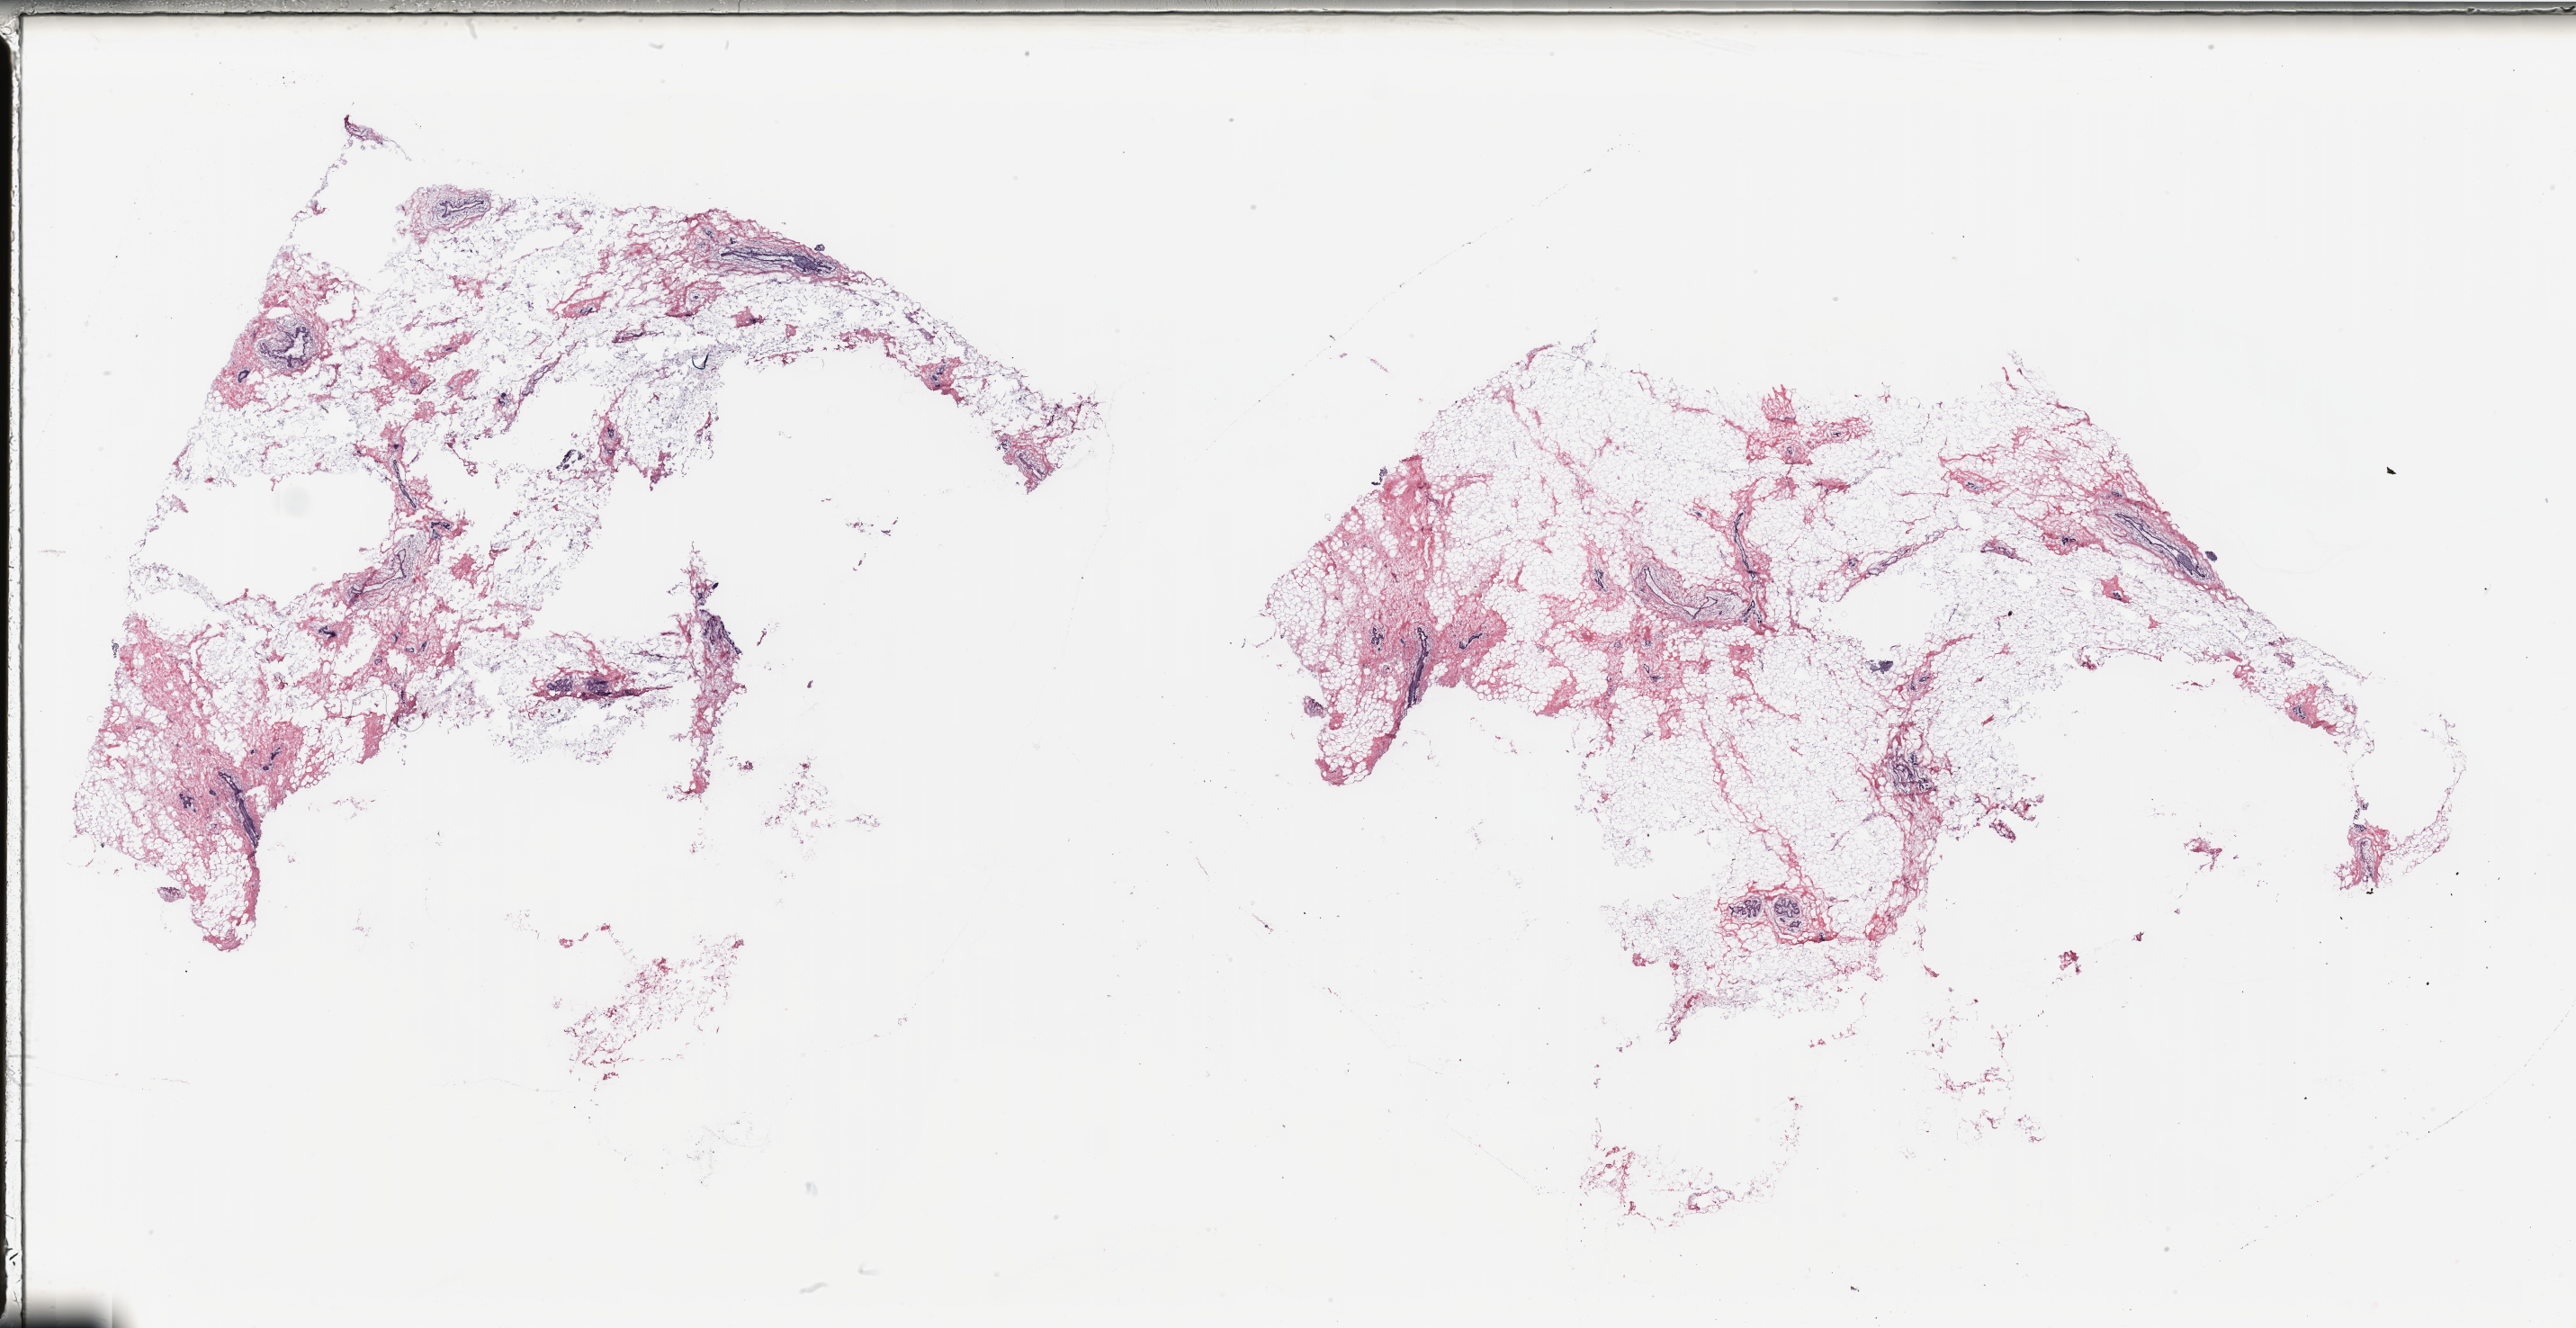
Digitized Hematoxylin and eosin (H&E) stained tissue section (whole slide), a low-resolution overview of the entire scanned area, about 45.3 x 23.3 mm (from a 20x scan), breast, tissue type not recorded. 54-year-old female patient.
- patient diagnosis: Infiltrating duct carcinoma, NOS